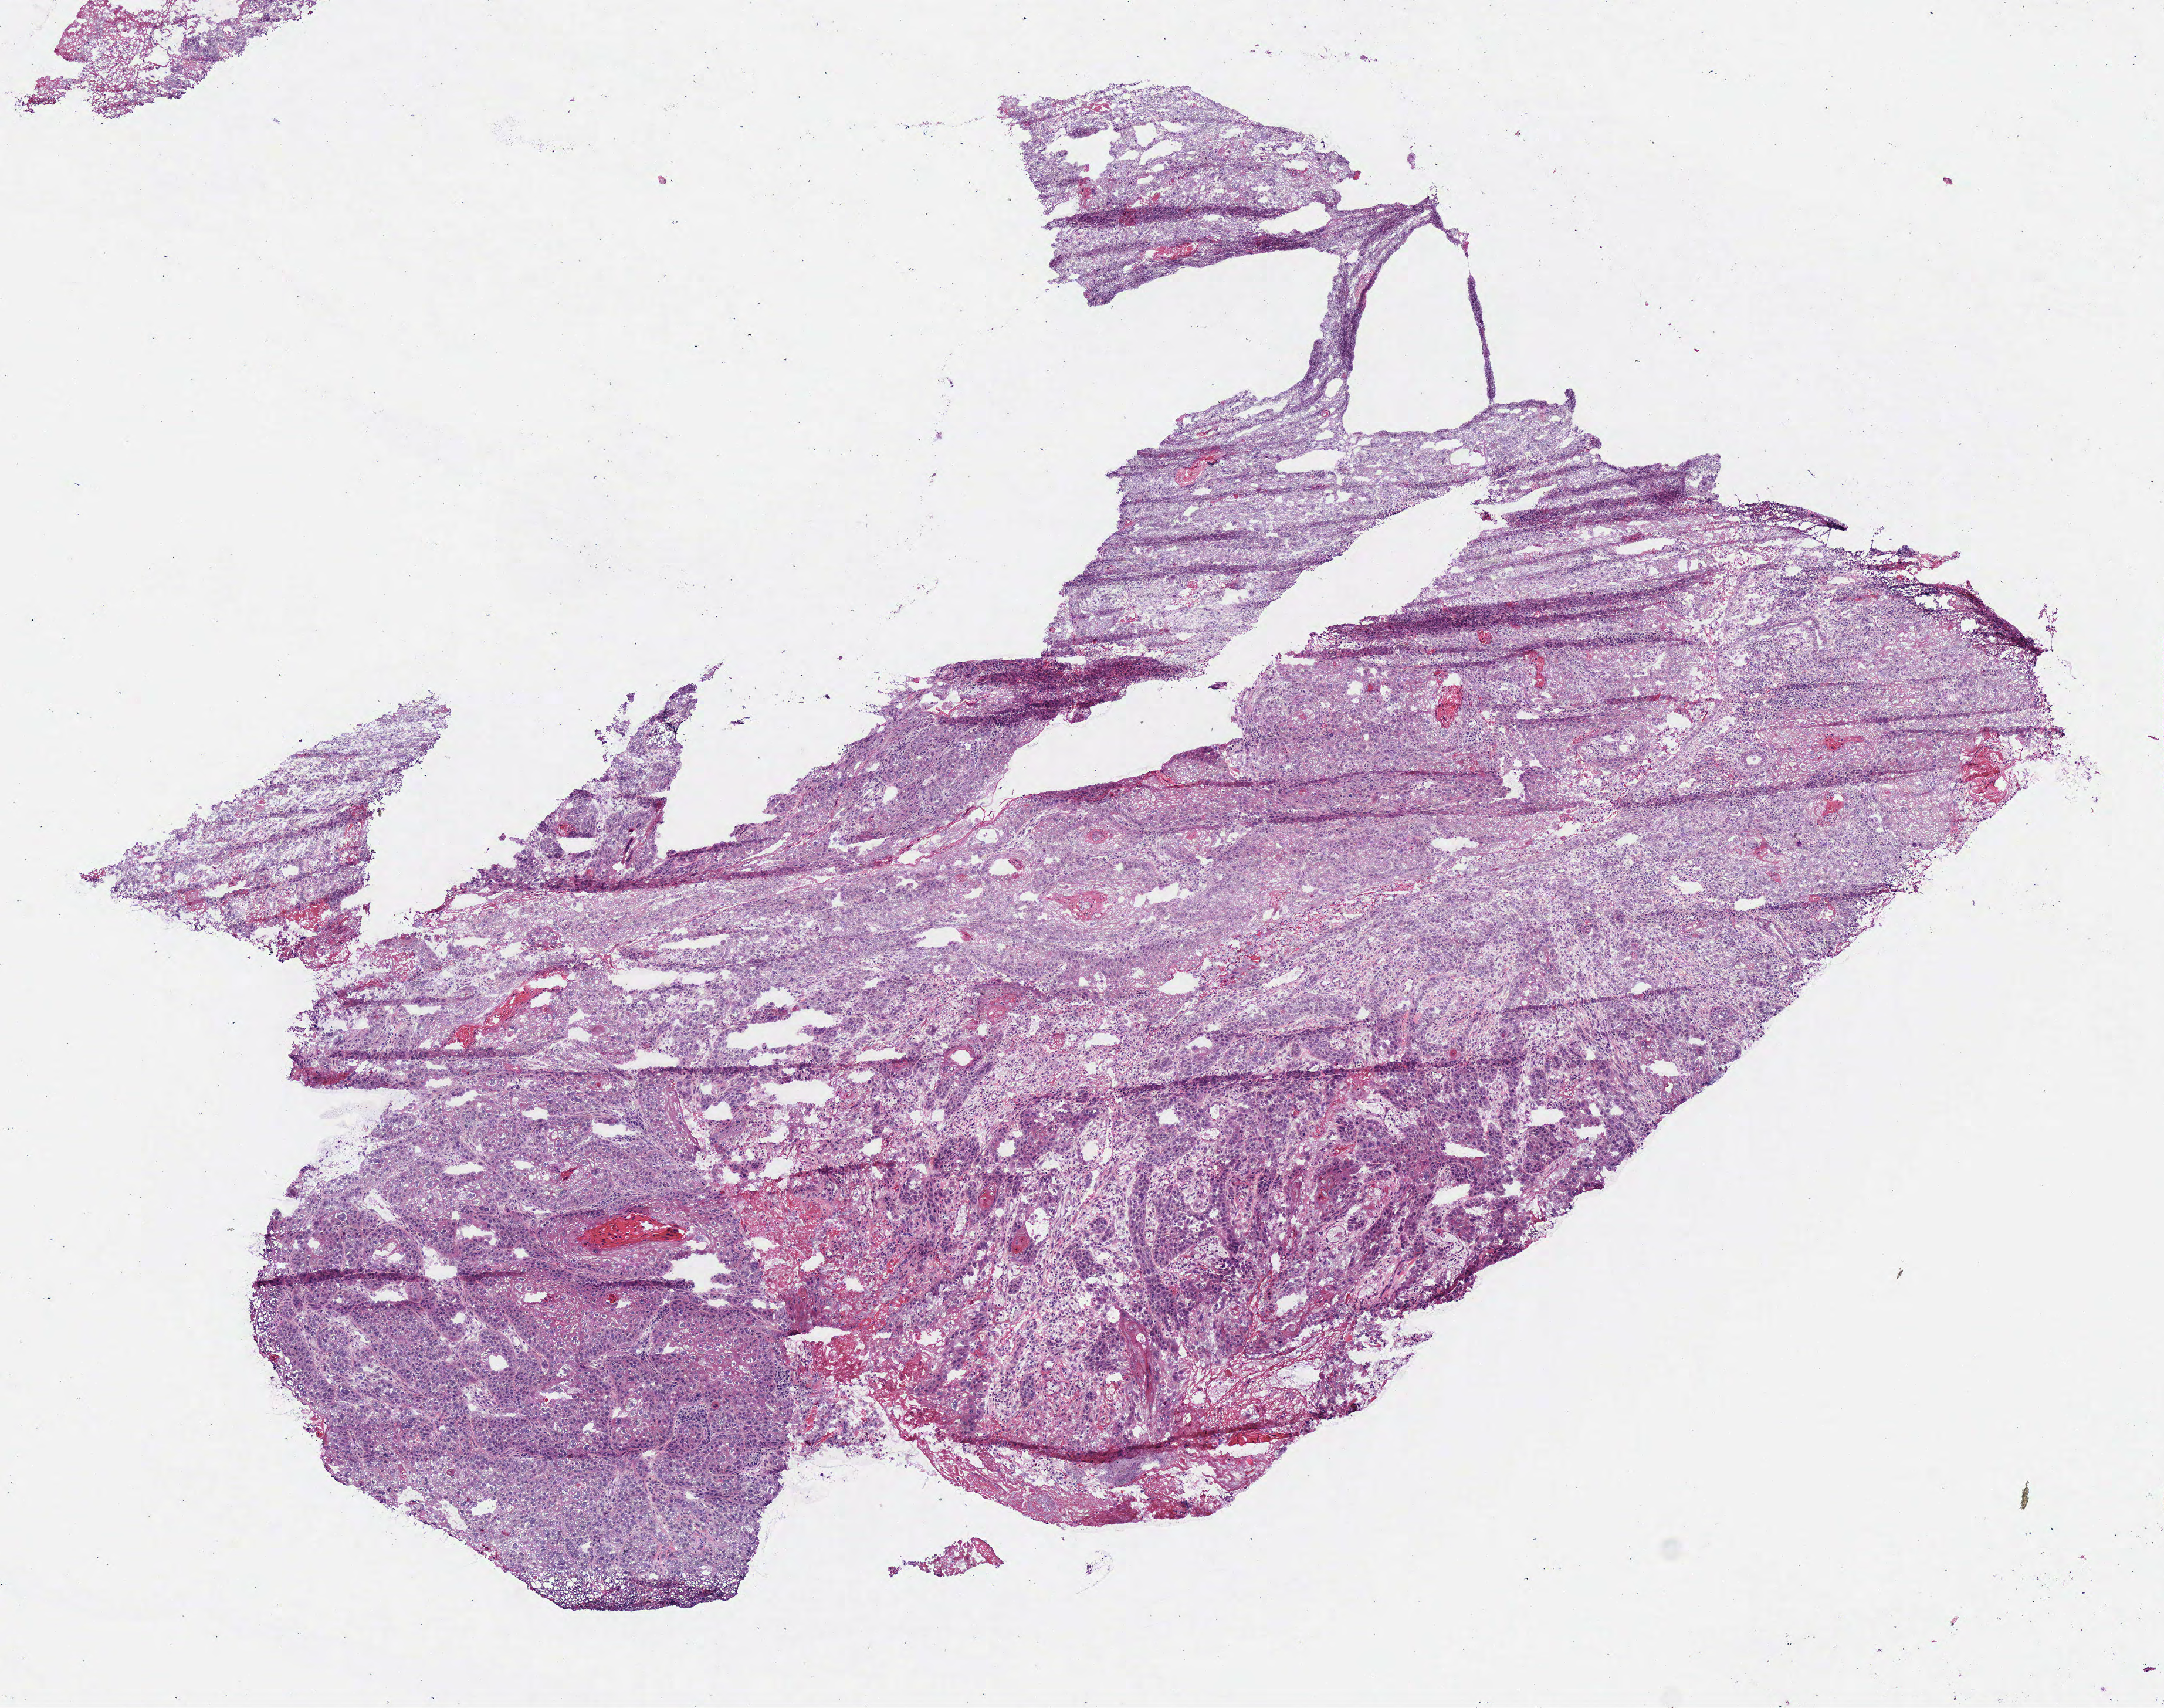
Whole-slide histology image, Hematoxylin and eosin (H&E) stained — whole scanned area (about 7.3 x 5.7 mm) shown as a low-resolution overview; frozen section; head and neck, primary tumour sample. Patient: male, age at initial diagnosis 47 years. Histologic grade: G2 (moderately differentiated). Slide review estimates, as recorded: tumour cells 98%, tumour nuclei 85%, necrosis 2%. Inflammatory infiltration, as recorded: lymphocyte infiltration 5%, neutrophil infiltration 2%.
* pathologic diagnosis: Squamous cell carcinoma, NOS (floor of mouth, NOS)
* laterality: midline
* AJCC pathologic stage: IVA (6th edition)
* TNM: T4a N2c